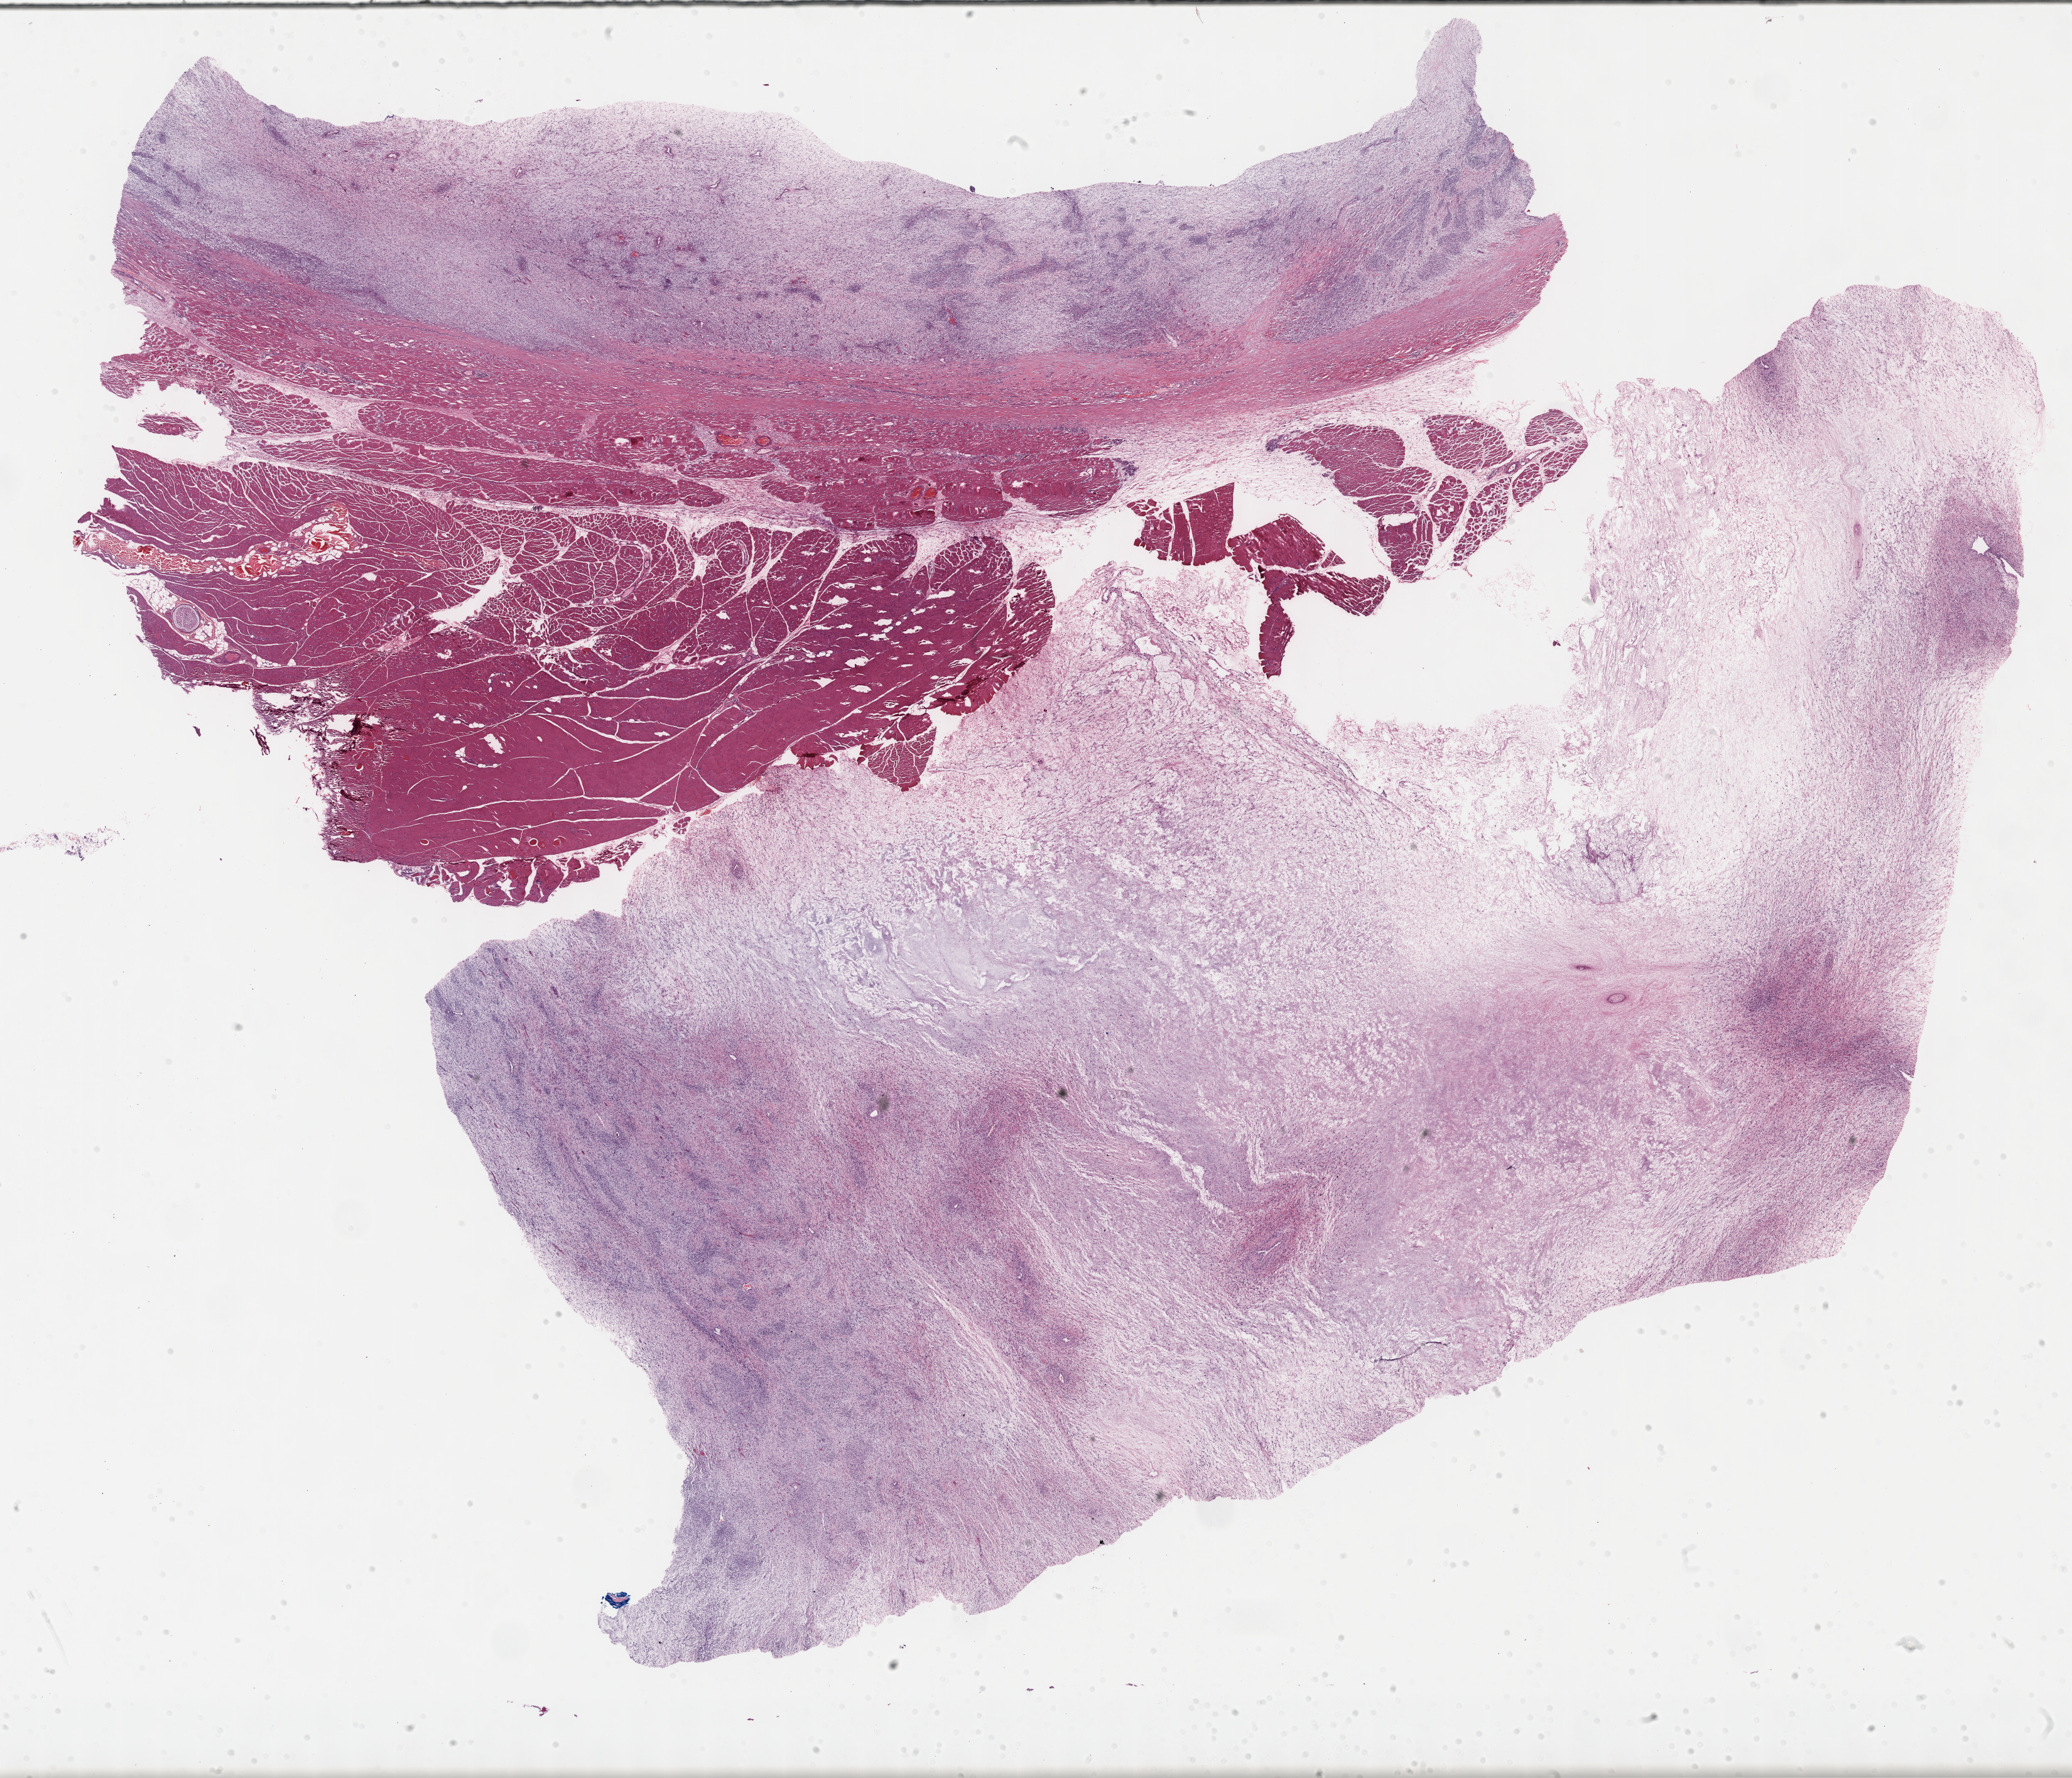
Digitized H&E tissue section (whole slide), whole scanned area (about 26.7 x 22.9 mm, from a 40x scan) shown as a low-resolution overview. Formalin-fixed paraffin-embedded (FFPE) diagnostic section. Sample: primary tumour, connective, subcutaneous and other soft tissues. Female, age 53 years at initial diagnosis.
- histologic diagnosis: Fibromyxosarcoma (connective, subcutaneous and other soft tissues of lower limb and hip)